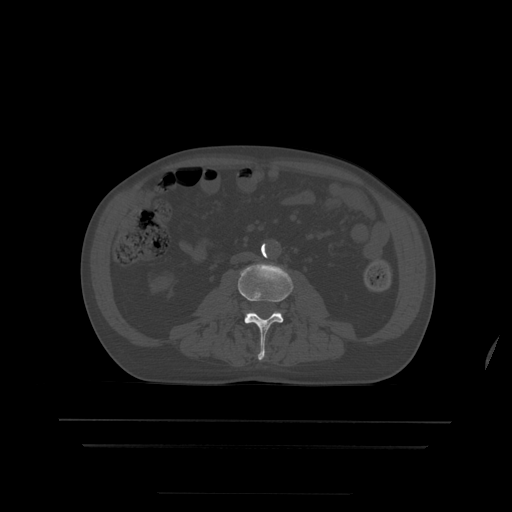
CT including the spine, one axial slice. Slice 116 of 522 in the series (ordered by position). Bone window (W 1800 / L 400 HU). 512 × 512 image matrix, field of view 436 × 436 mm. Patient age 68 years. Case-level facts recorded for this patient, not image findings: primary cancer: urothelial.
Structures marked on this image (semi-automatically segmented with operator editing):
- L3 vertebra: bounding box <238,263,293,361> (left, top, right, bottom; pixels)